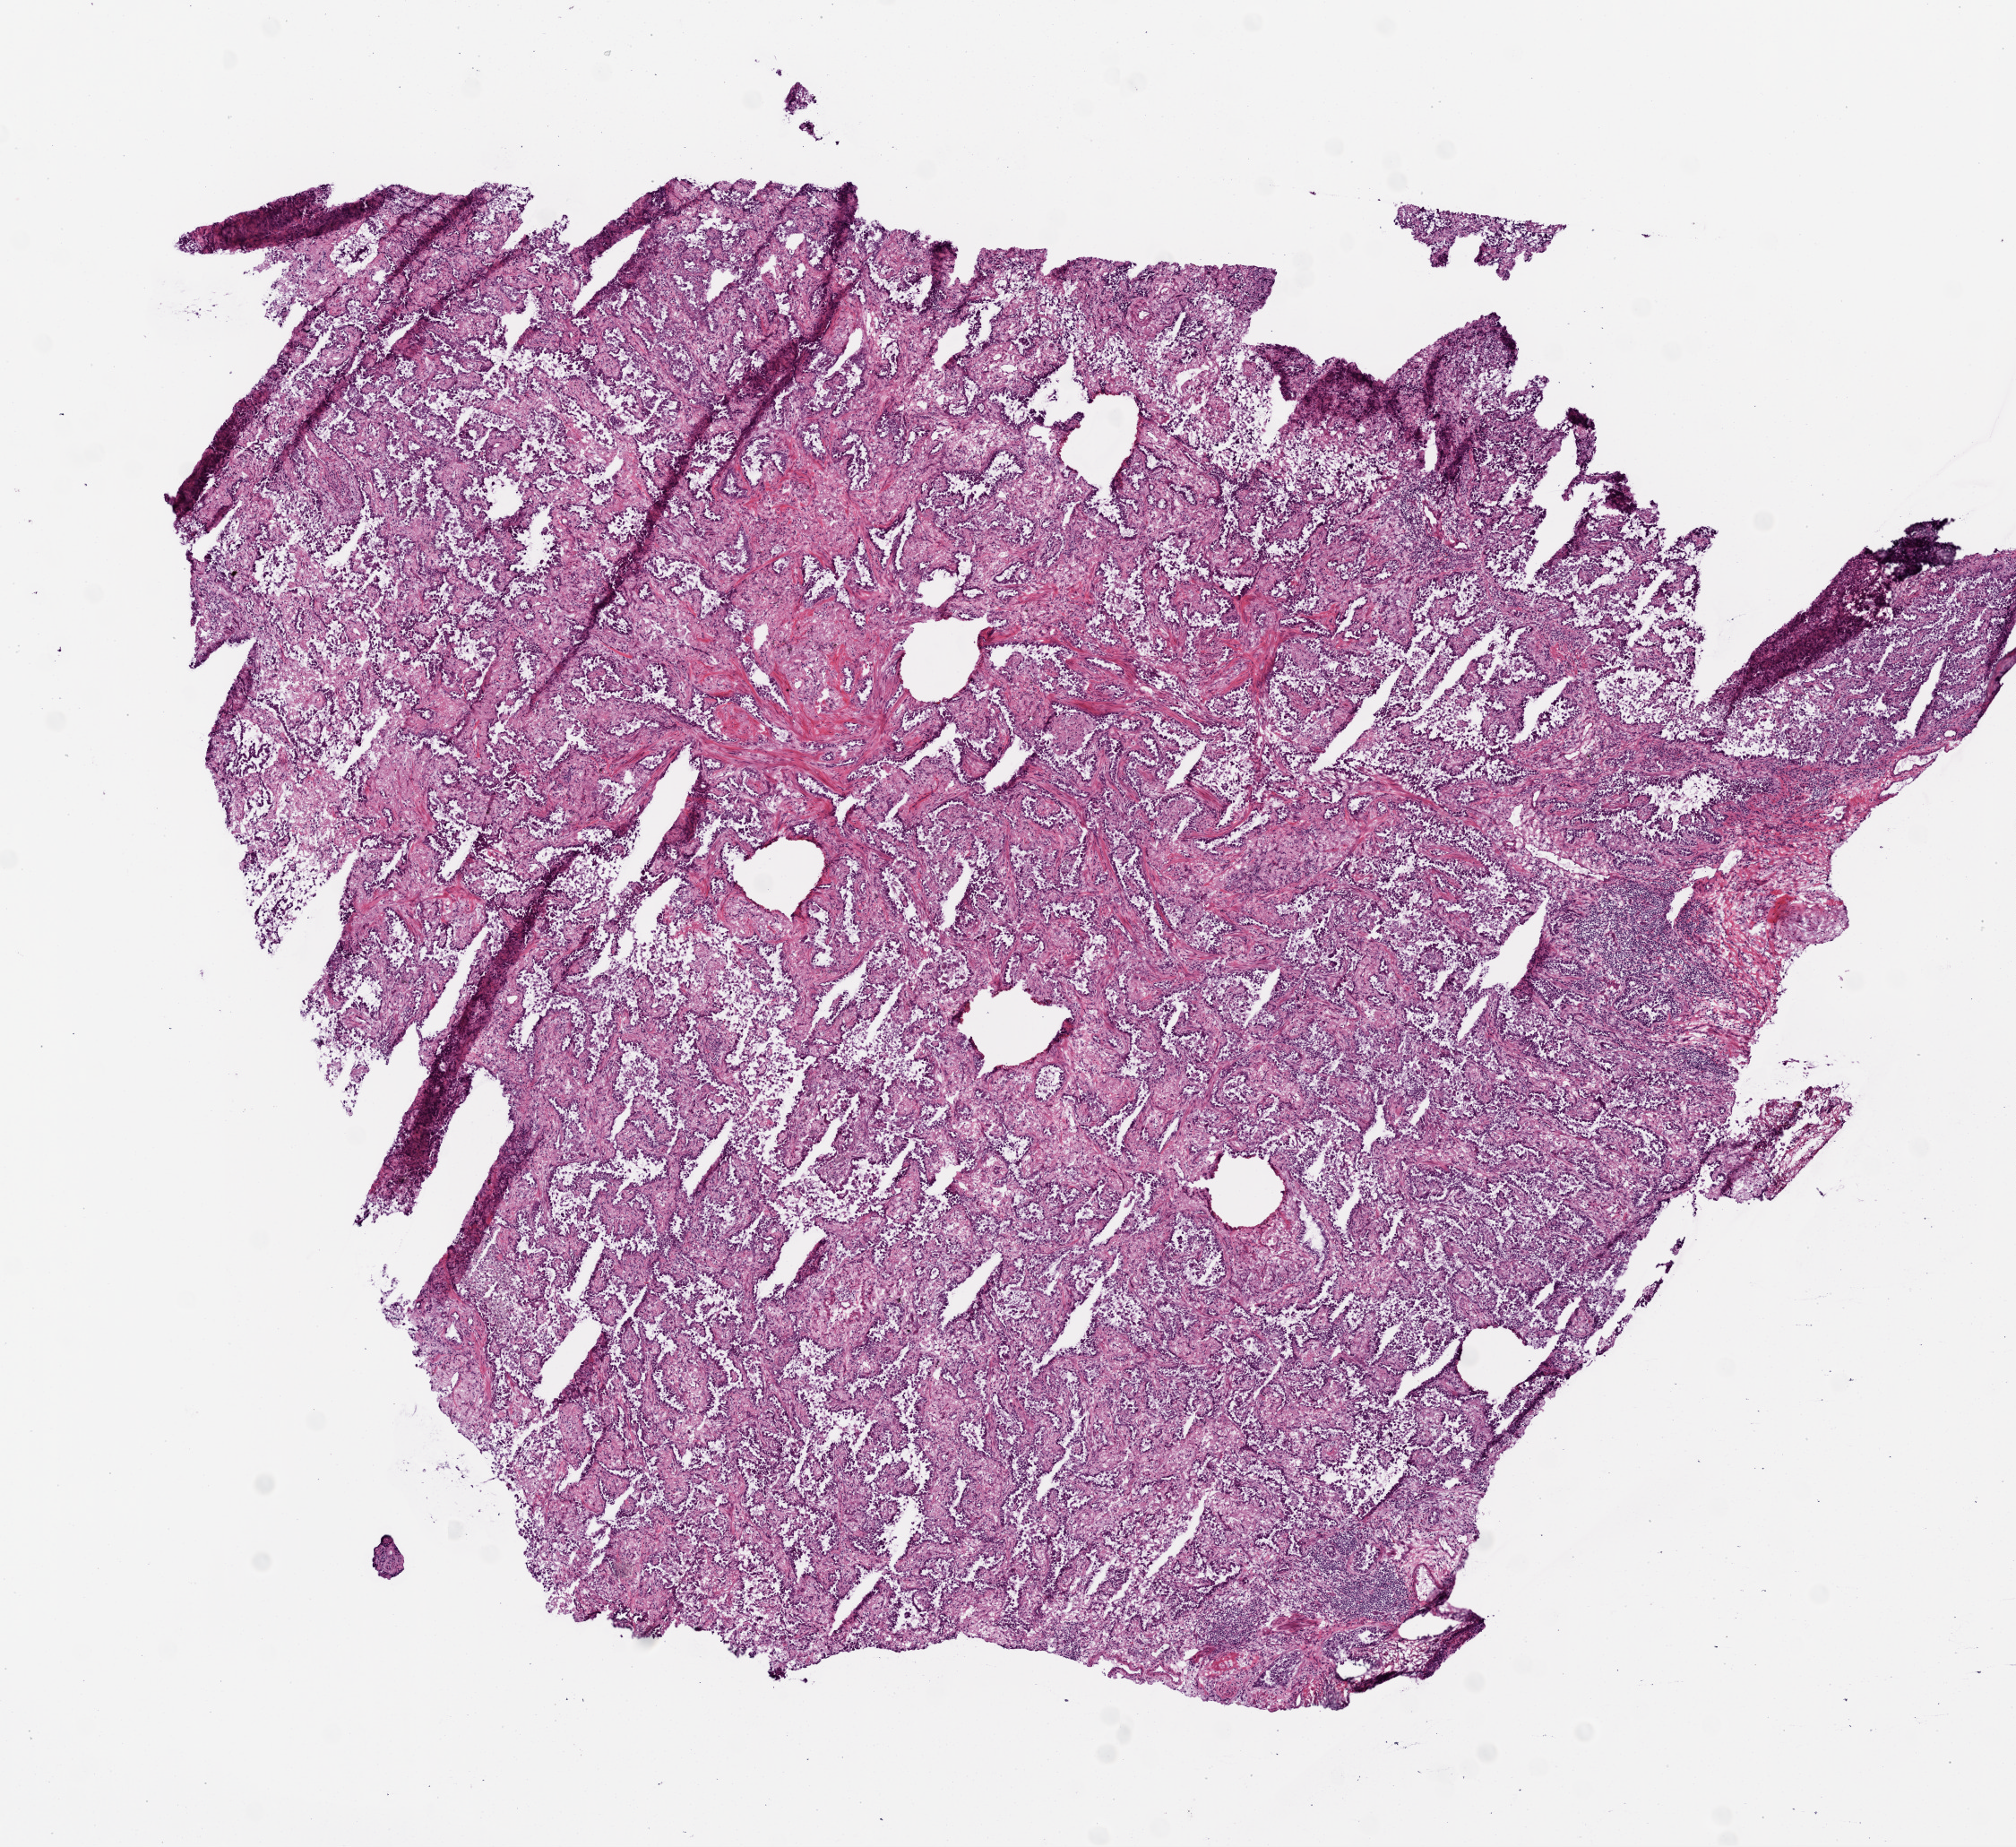
Whole-slide histology image, H&E-stained, shown as a low-resolution overview of the whole scanned area (about 9.0 x 8.3 mm, acquisition: 20x scan). Frozen section. Sample: primary tumour, lung. Female patient; age at initial diagnosis 59 years. Pathologist review of this section (percent, as recorded): tumour cells 100%, tumour nuclei 80%.
Histologic diagnosis: Adenocarcinoma with mixed subtypes (lower lobe, lung).